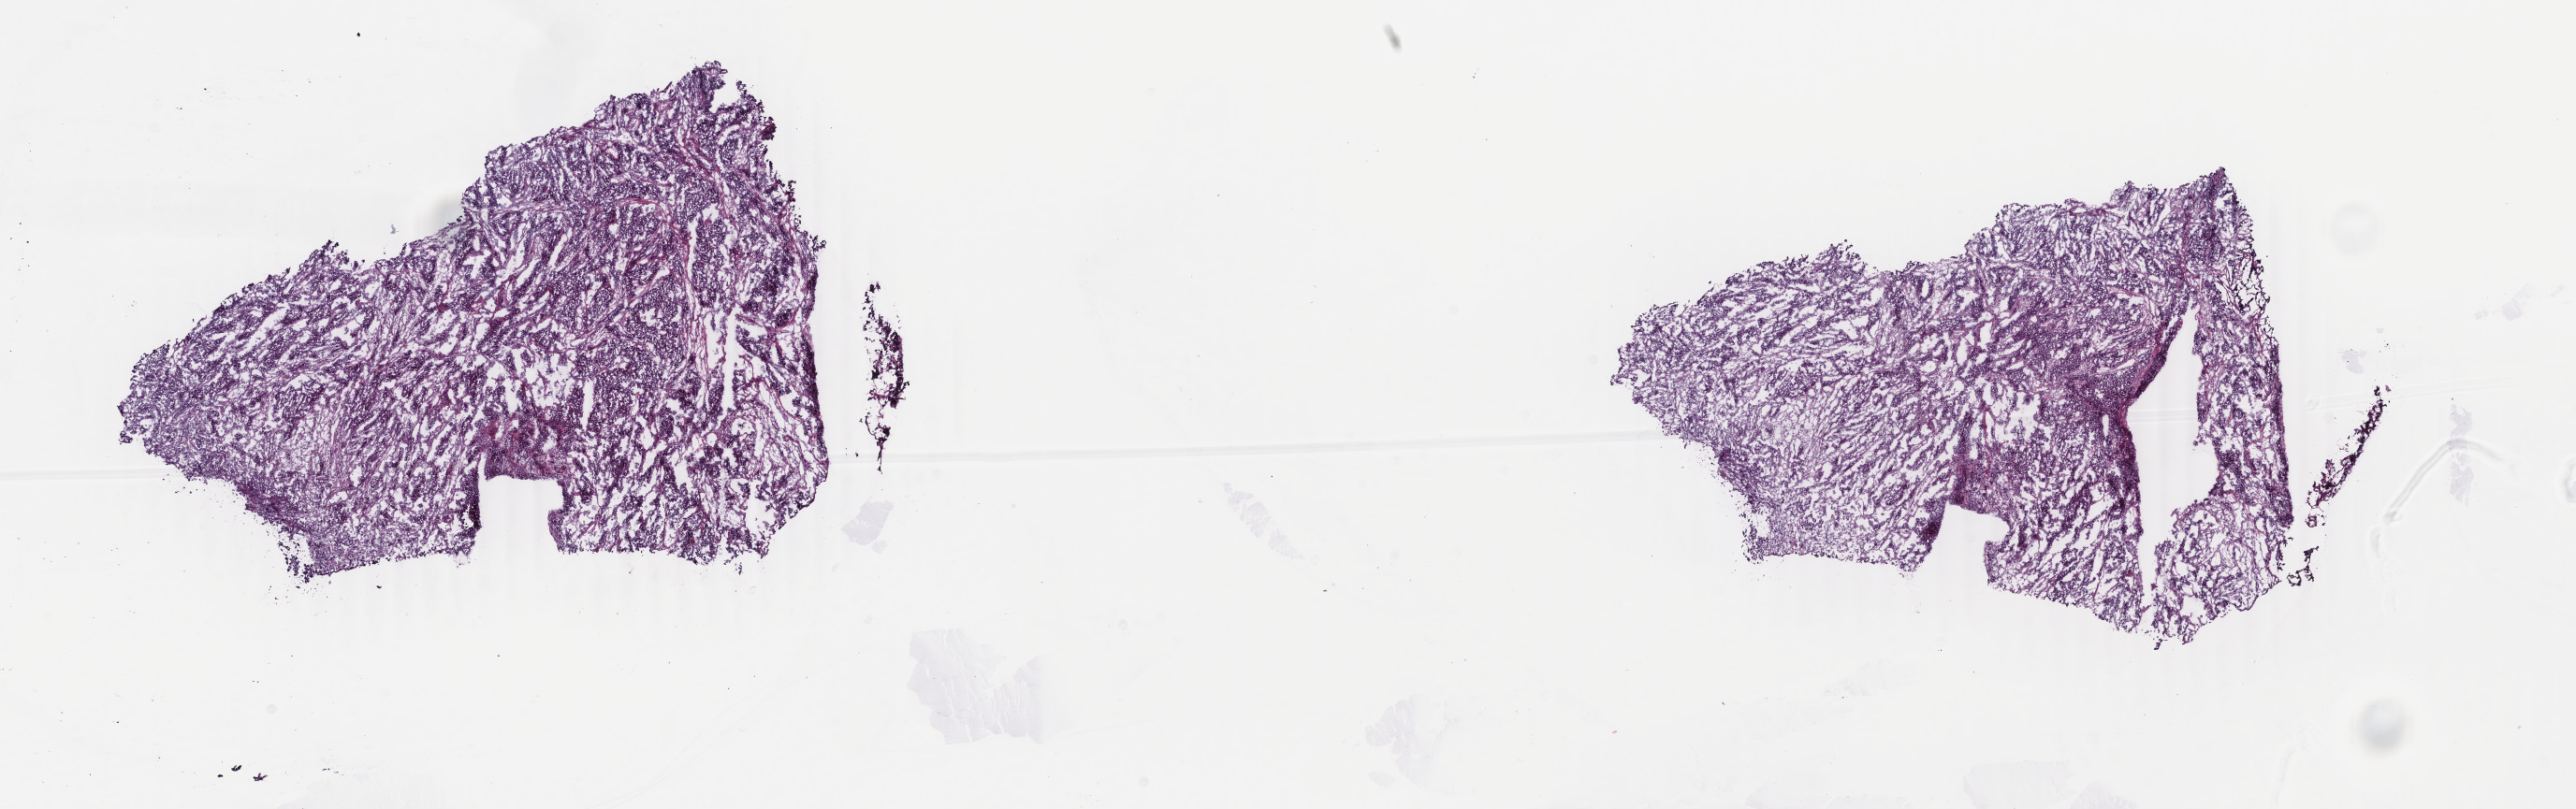
Whole-slide histology image, H&E-stained, whole scanned area (about 21.9 x 6.9 mm, from a 40x scan) shown as a low-resolution overview. Frozen section from the top of the tissue portion. Sample: primary tumour, bladder. Male patient; age at initial diagnosis 72 years. Histologic grade: high grade. Composition of this section per pathologist review: tumour cells 90%, tumour nuclei 90%, normal cells 0%, stromal cells 10%, necrosis 0%. Inflammatory infiltration, as recorded: lymphocyte infiltration 2%, monocyte infiltration 1%, neutrophil infiltration 1%.
• AJCC pathologic stage: III (6th edition)
• lymph nodes positive (case pathology): 0 of 22 examined
• pathologic diagnosis: Transitional cell carcinoma